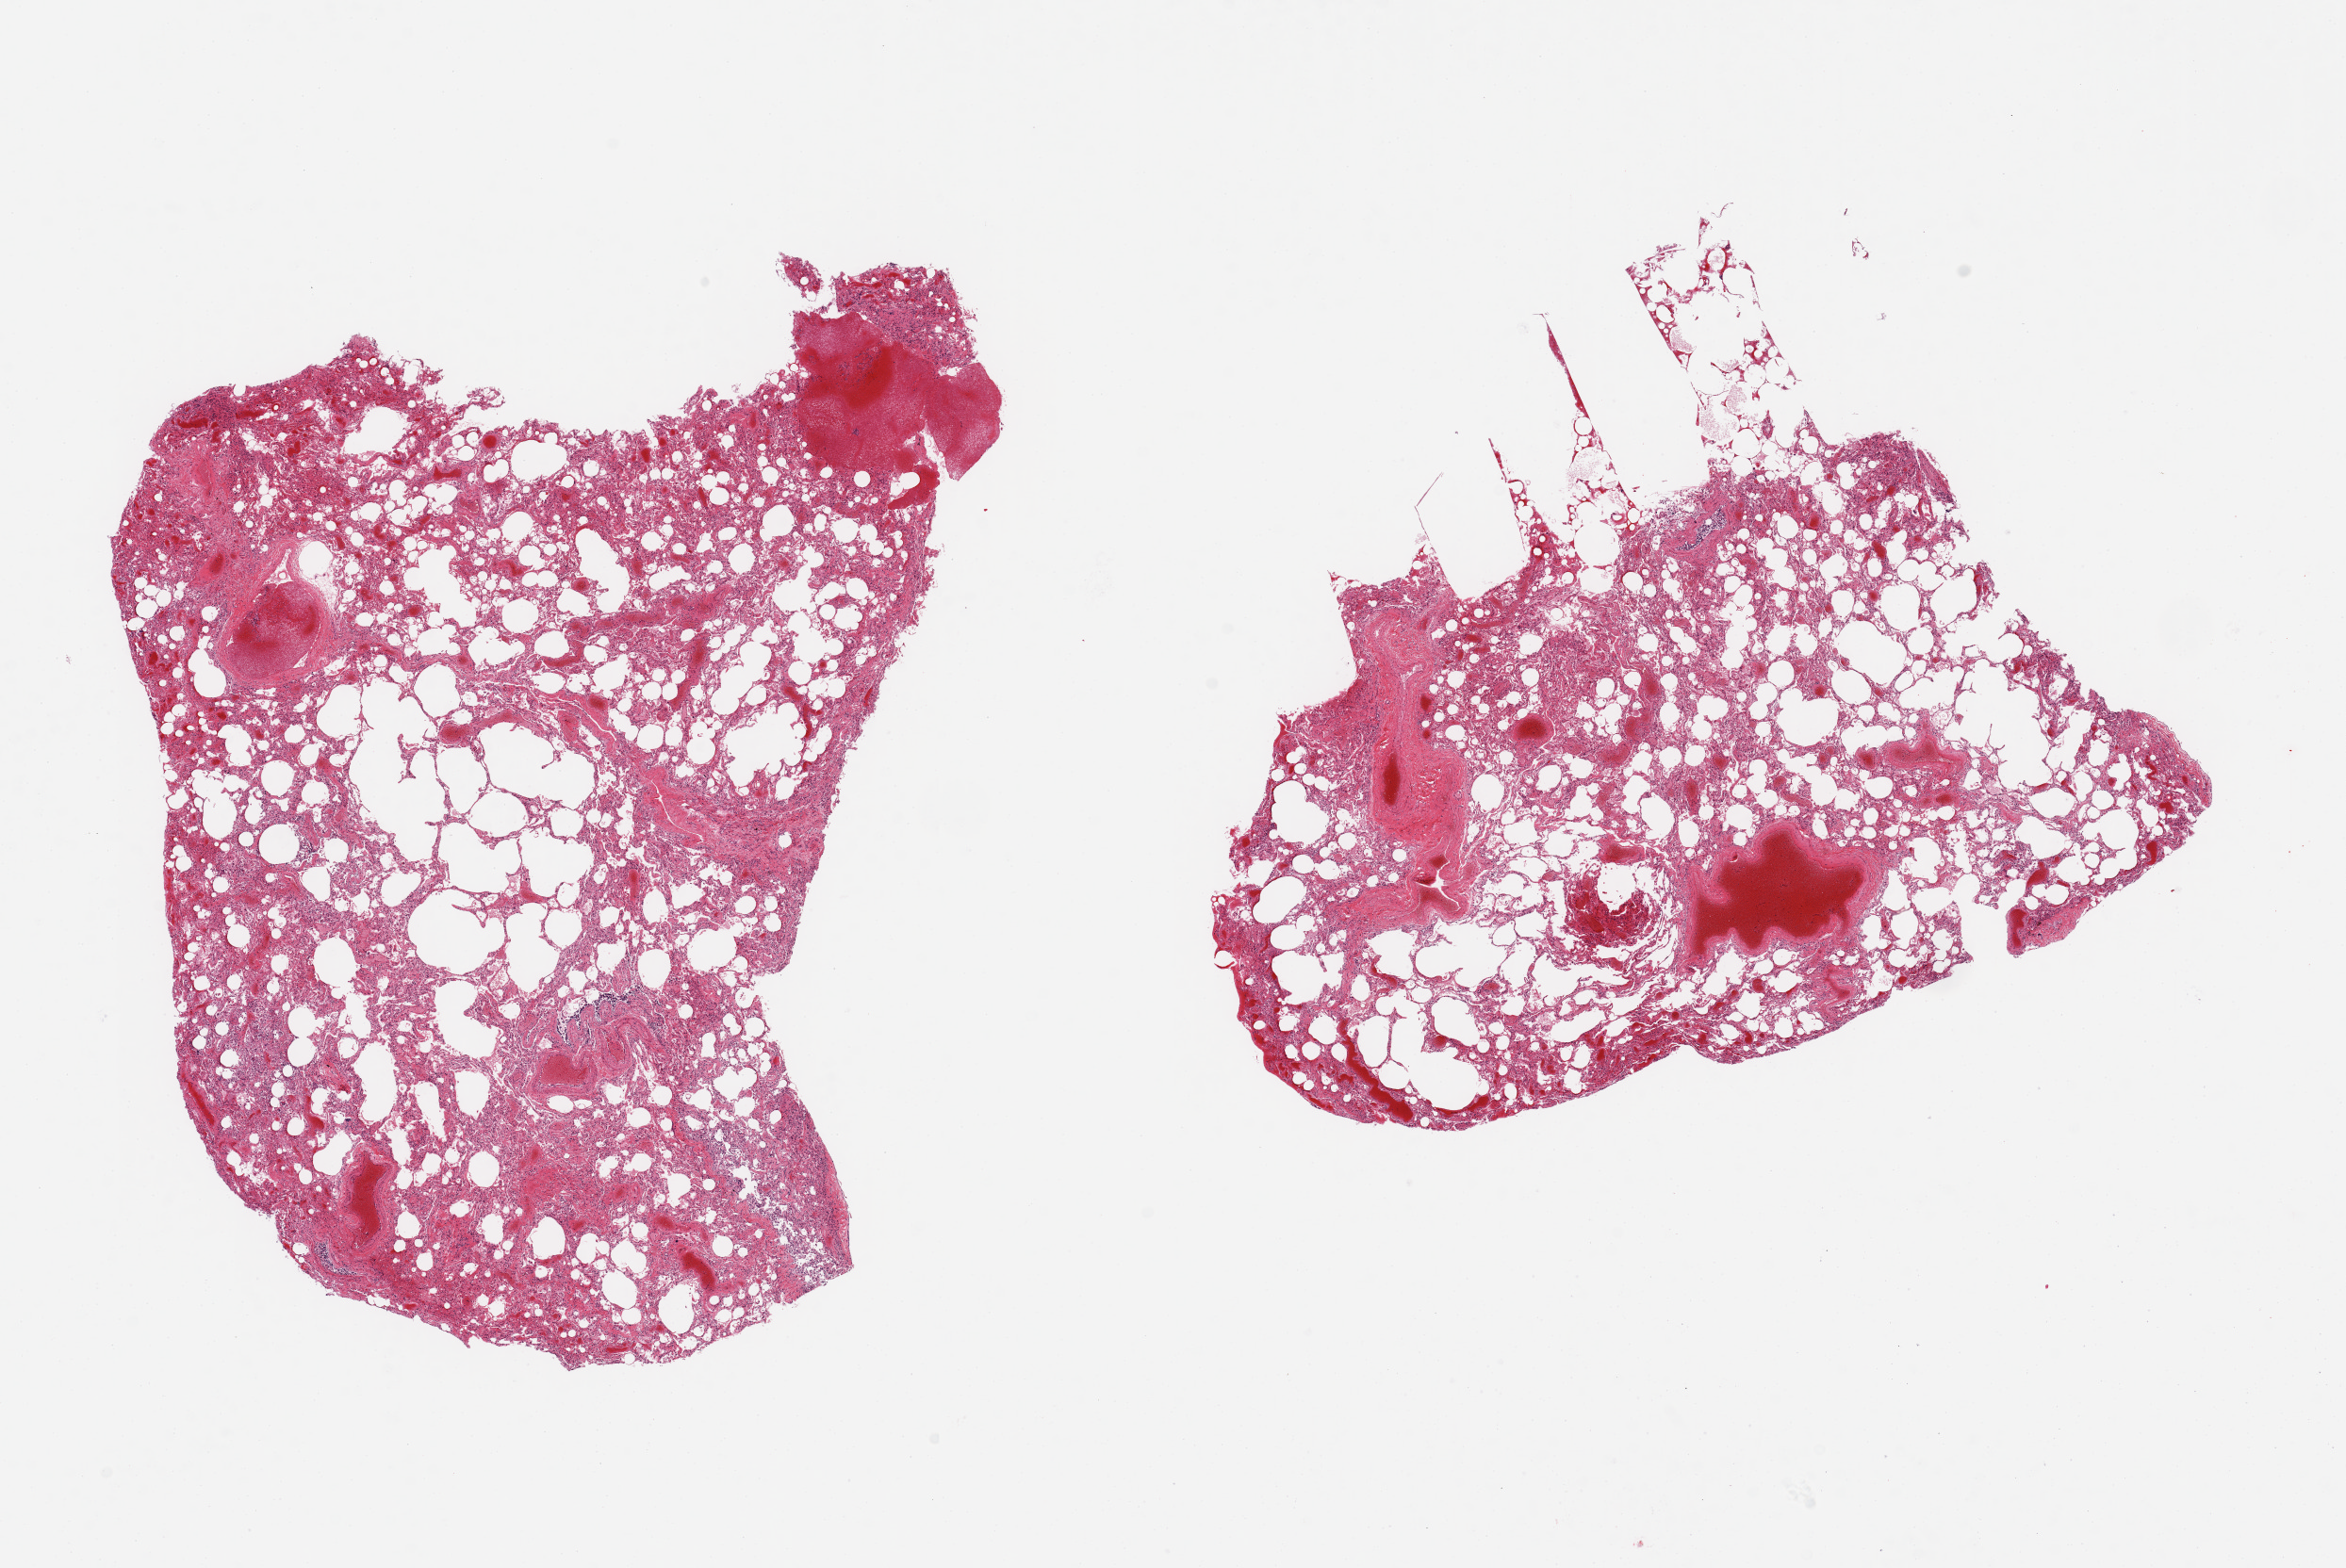
Digitized haematoxylin and eosin-stained section, shown as a low-resolution overview of the whole scanned area (about 19.7 x 13.2 mm, acquisition: 20x scan), PAXgene-fixed paraffin-embedded (PFPE) section, section of lung (target tissue), tissue donor sample. Female donor.
Reviewer comment on this tissue sample: 2 pieces; moderate emphysema; focal hemorrhage; congested vessels.